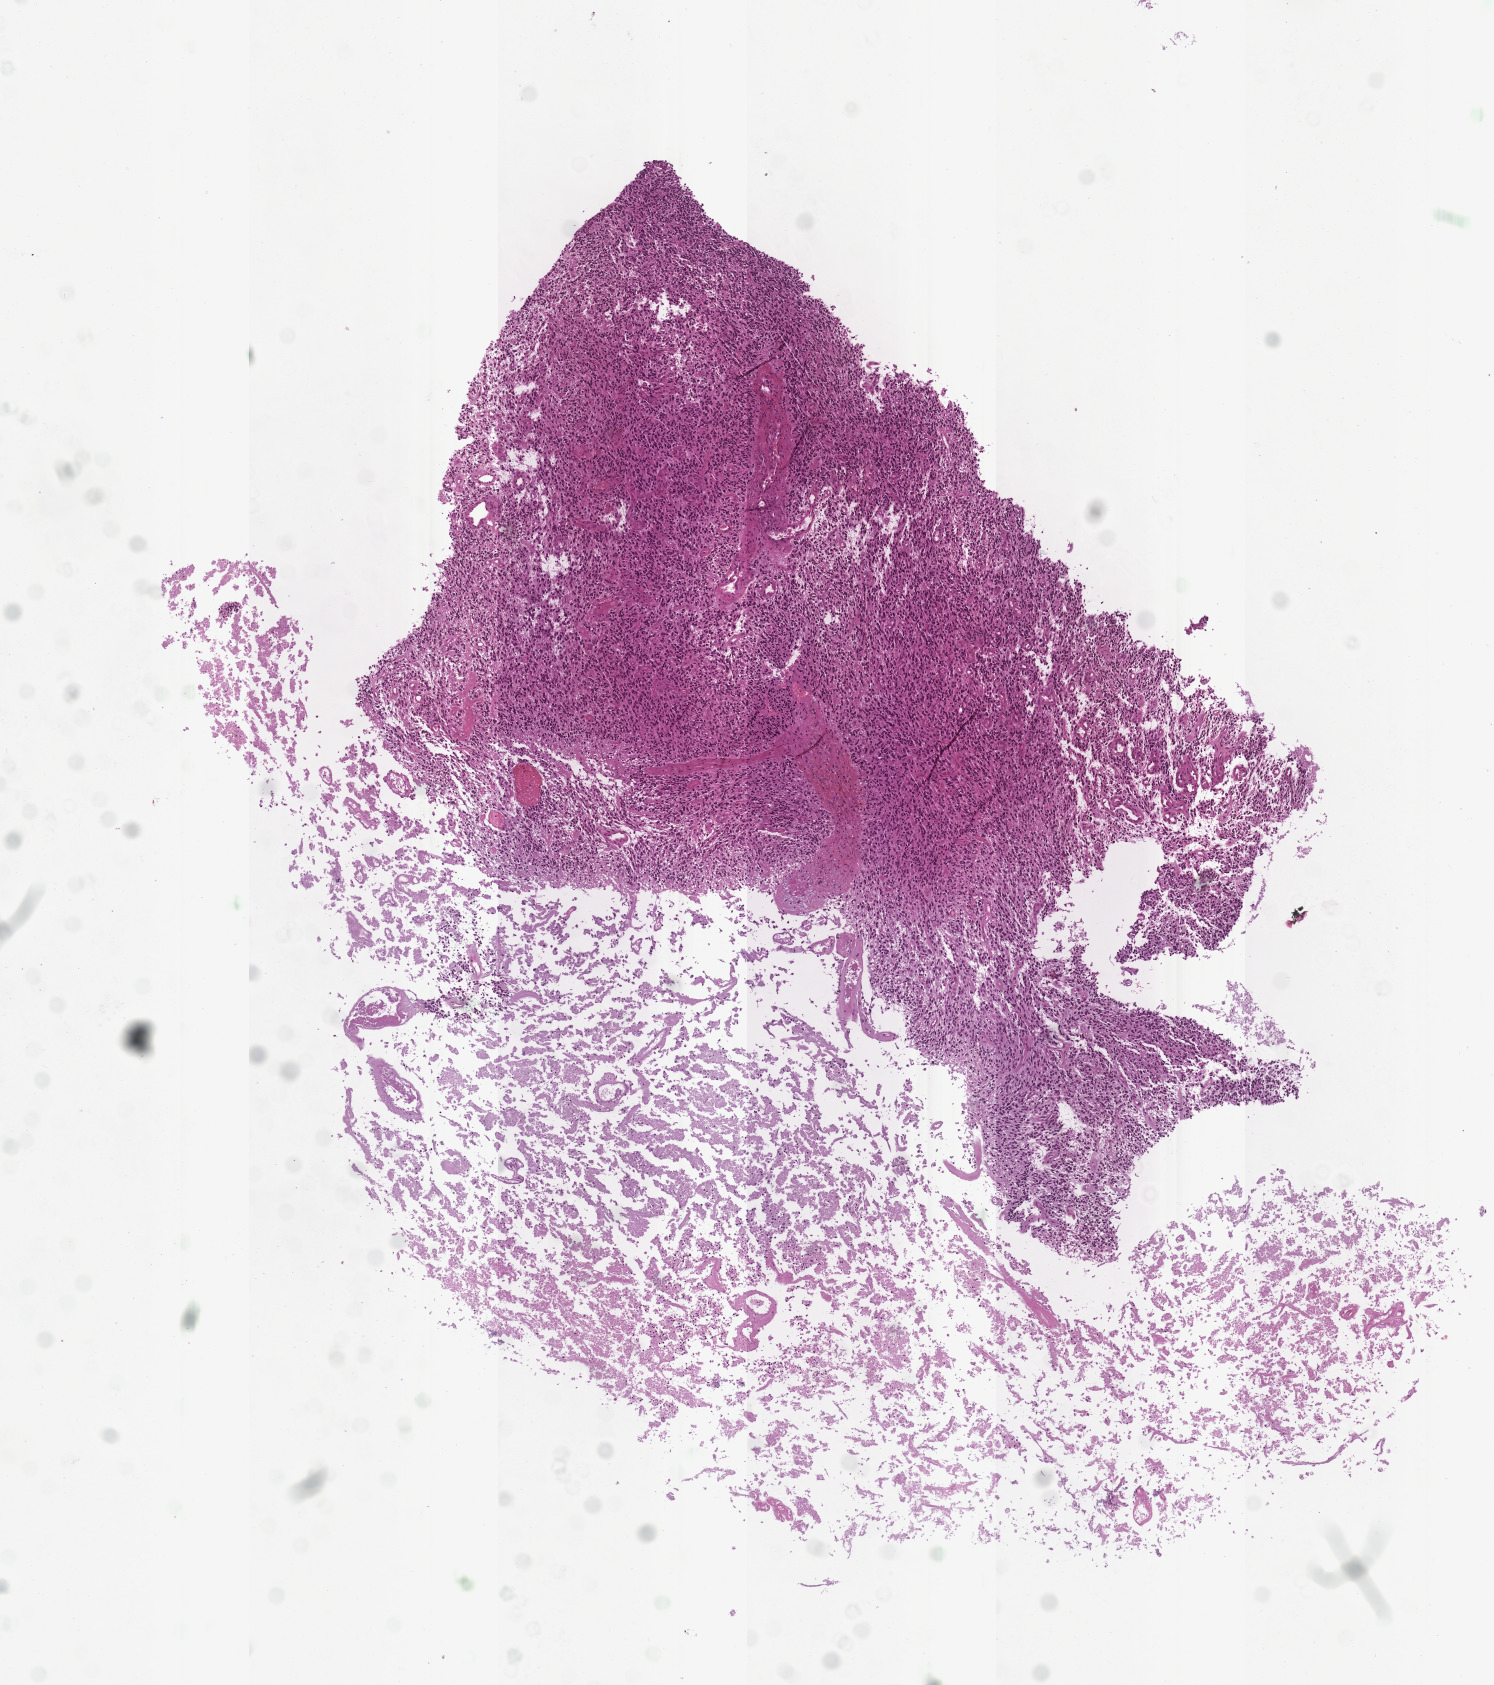
Whole-slide histology image, H&E-stained — low-resolution overview of the scanned area, about 6.0 x 6.8 mm (slide scanned at 20x); brain, tumour tissue. Male, 44 y/o.
Histologic diagnosis: Glioblastoma.